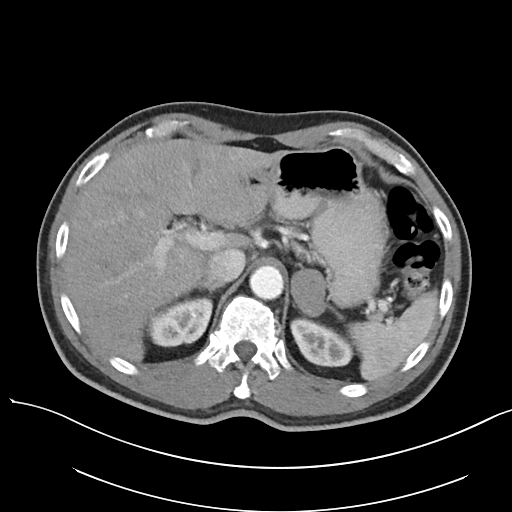
Contrast-enhanced abdominal CT, one axial slice; position 80 of 138 along the scan axis; 120 kVp; intravenous contrast given; soft-tissue window (W 400 / L 40 HU); 512 × 512 image matrix, field of view 400 × 400 mm. Male patient, age 63 years. From the clinical record (not read from this slice): diagnosis: adrenocortical carcinoma; tumour side: left adrenal; tumour size at pathology: 4.5 cm; Ki-67 index: 12 %; stage (as recorded): 1.
Outlined on this slice (semi-automatic segmentation, software-assisted and operator-edited):
- mass: bounding box [x1, y1, x2, y2] px = [291, 269, 326, 316]